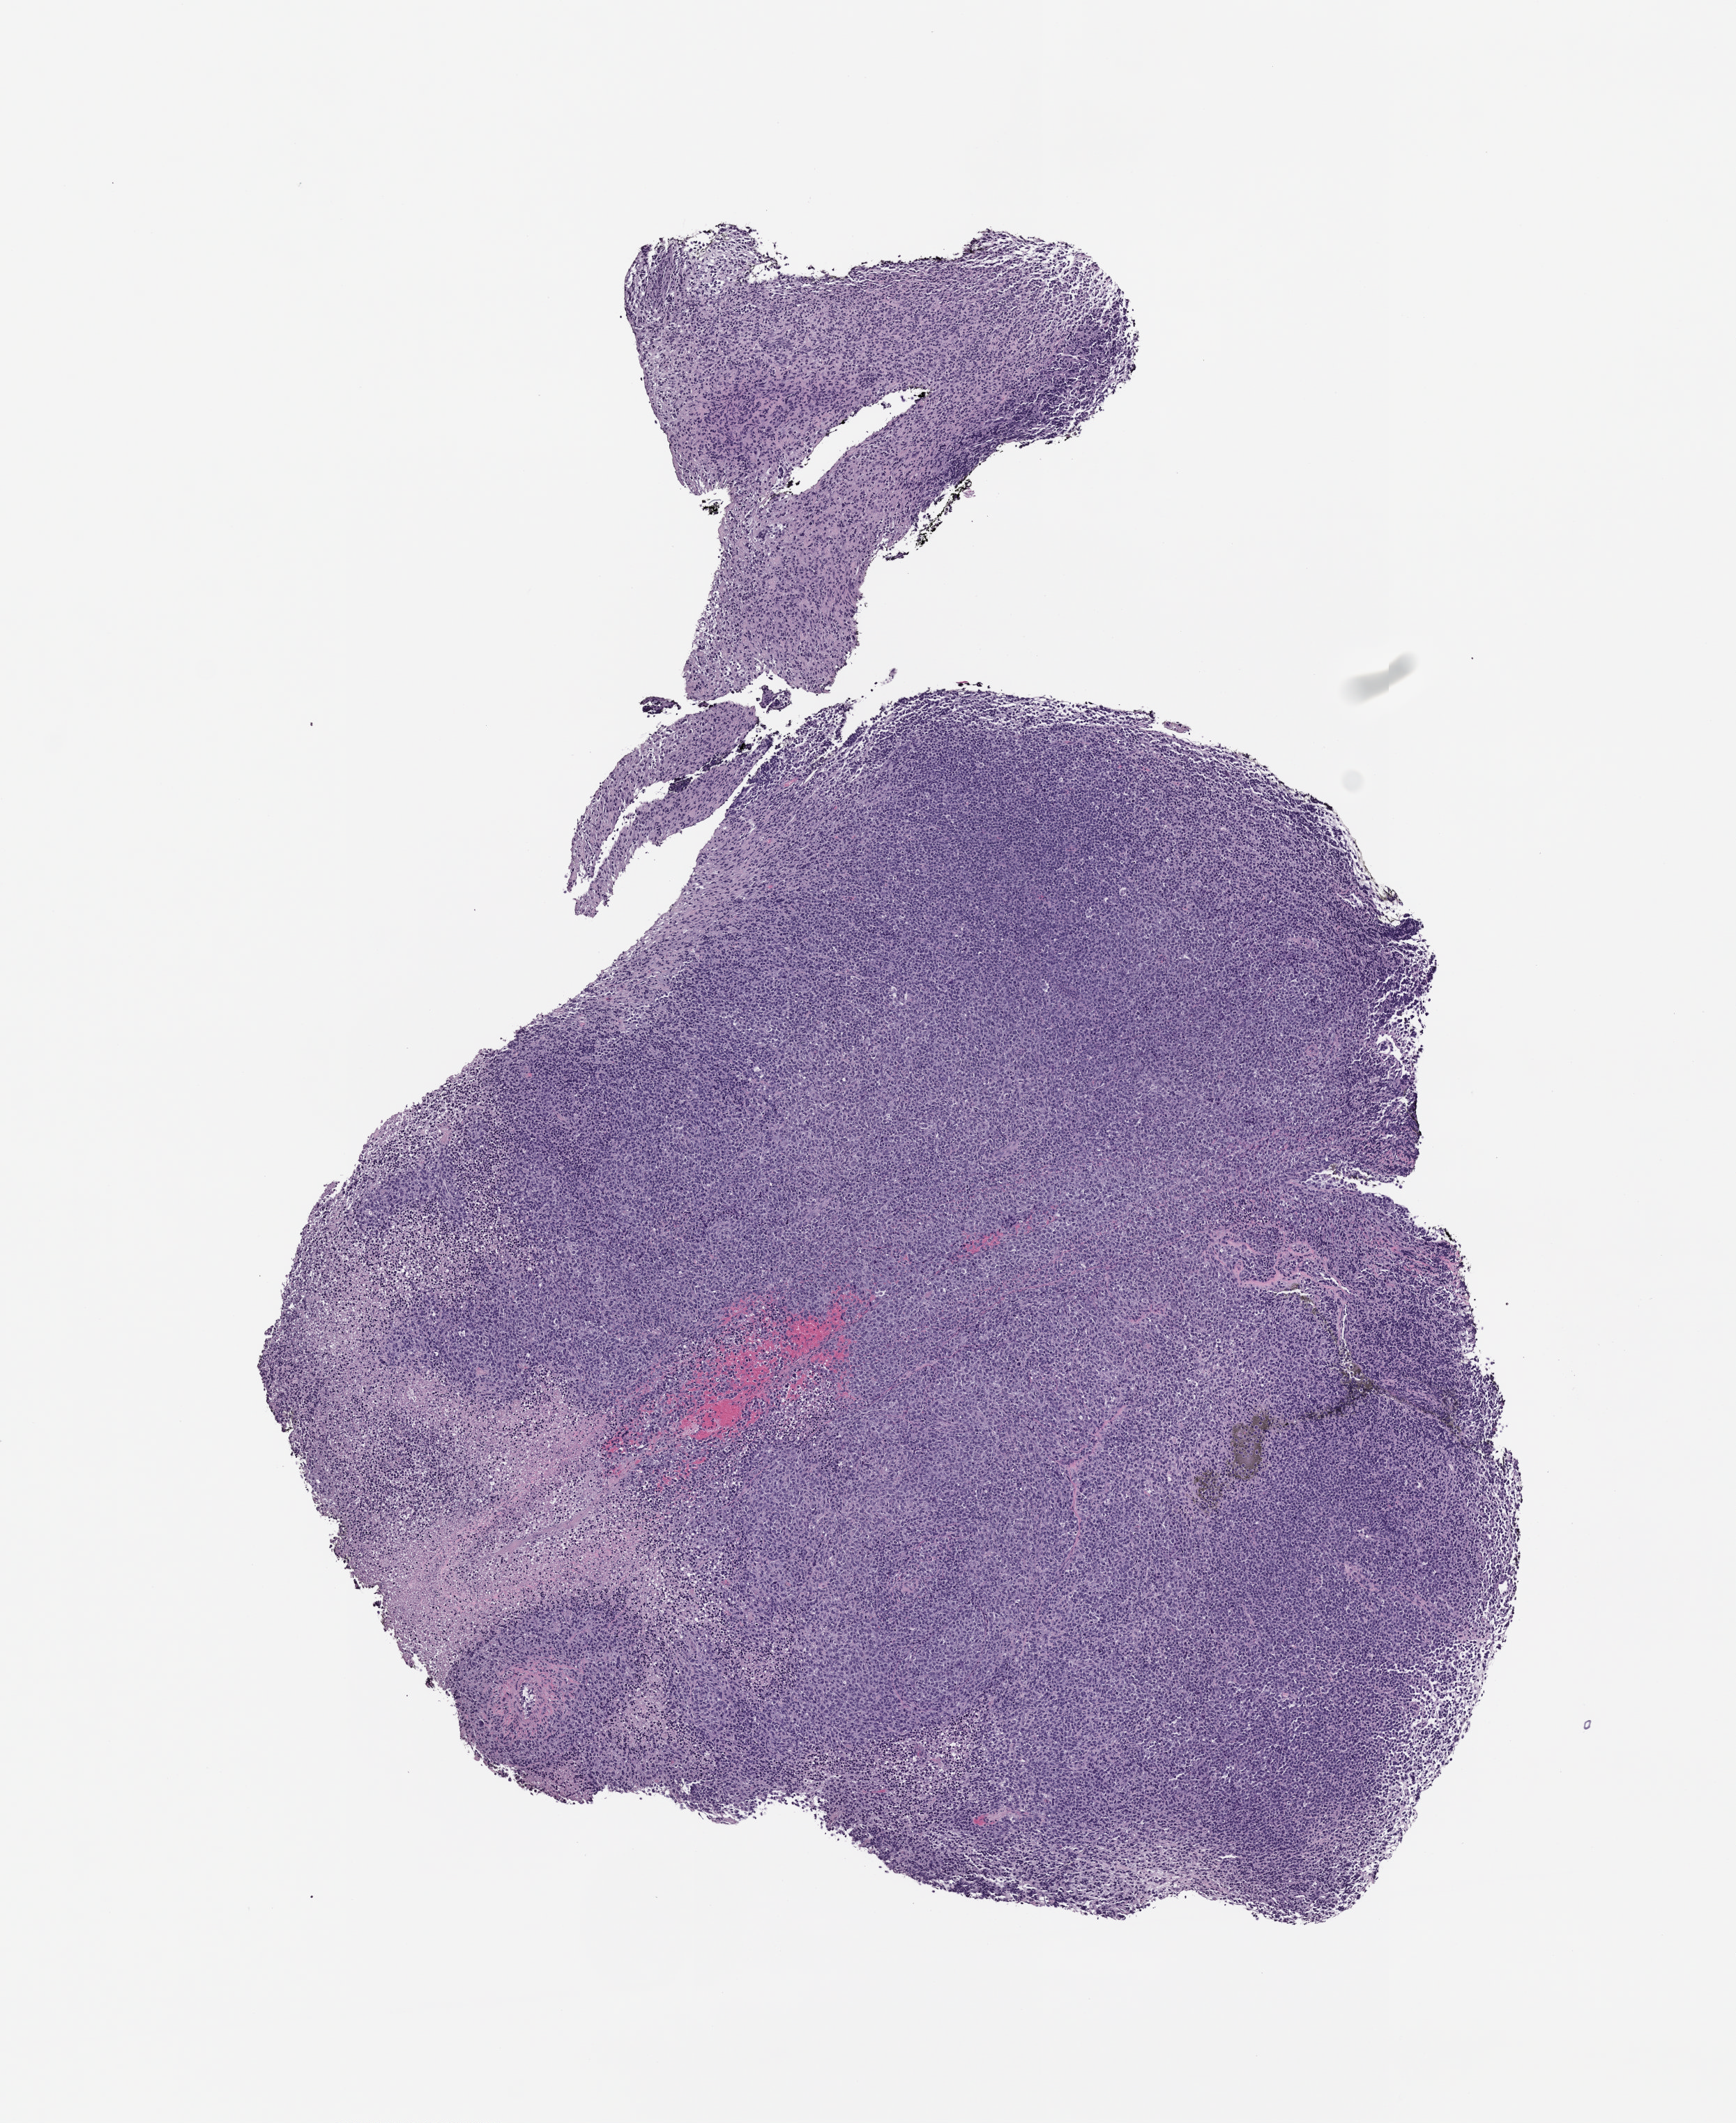
Whole-slide image, hematoxylin and eosin (H&E): patient-derived xenograft (human tumor grown in a mouse), a low-resolution overview of the entire scanned area, about 5.0 x 6.1 mm.
Specimen: formalin-fixed paraffin-embedded section.